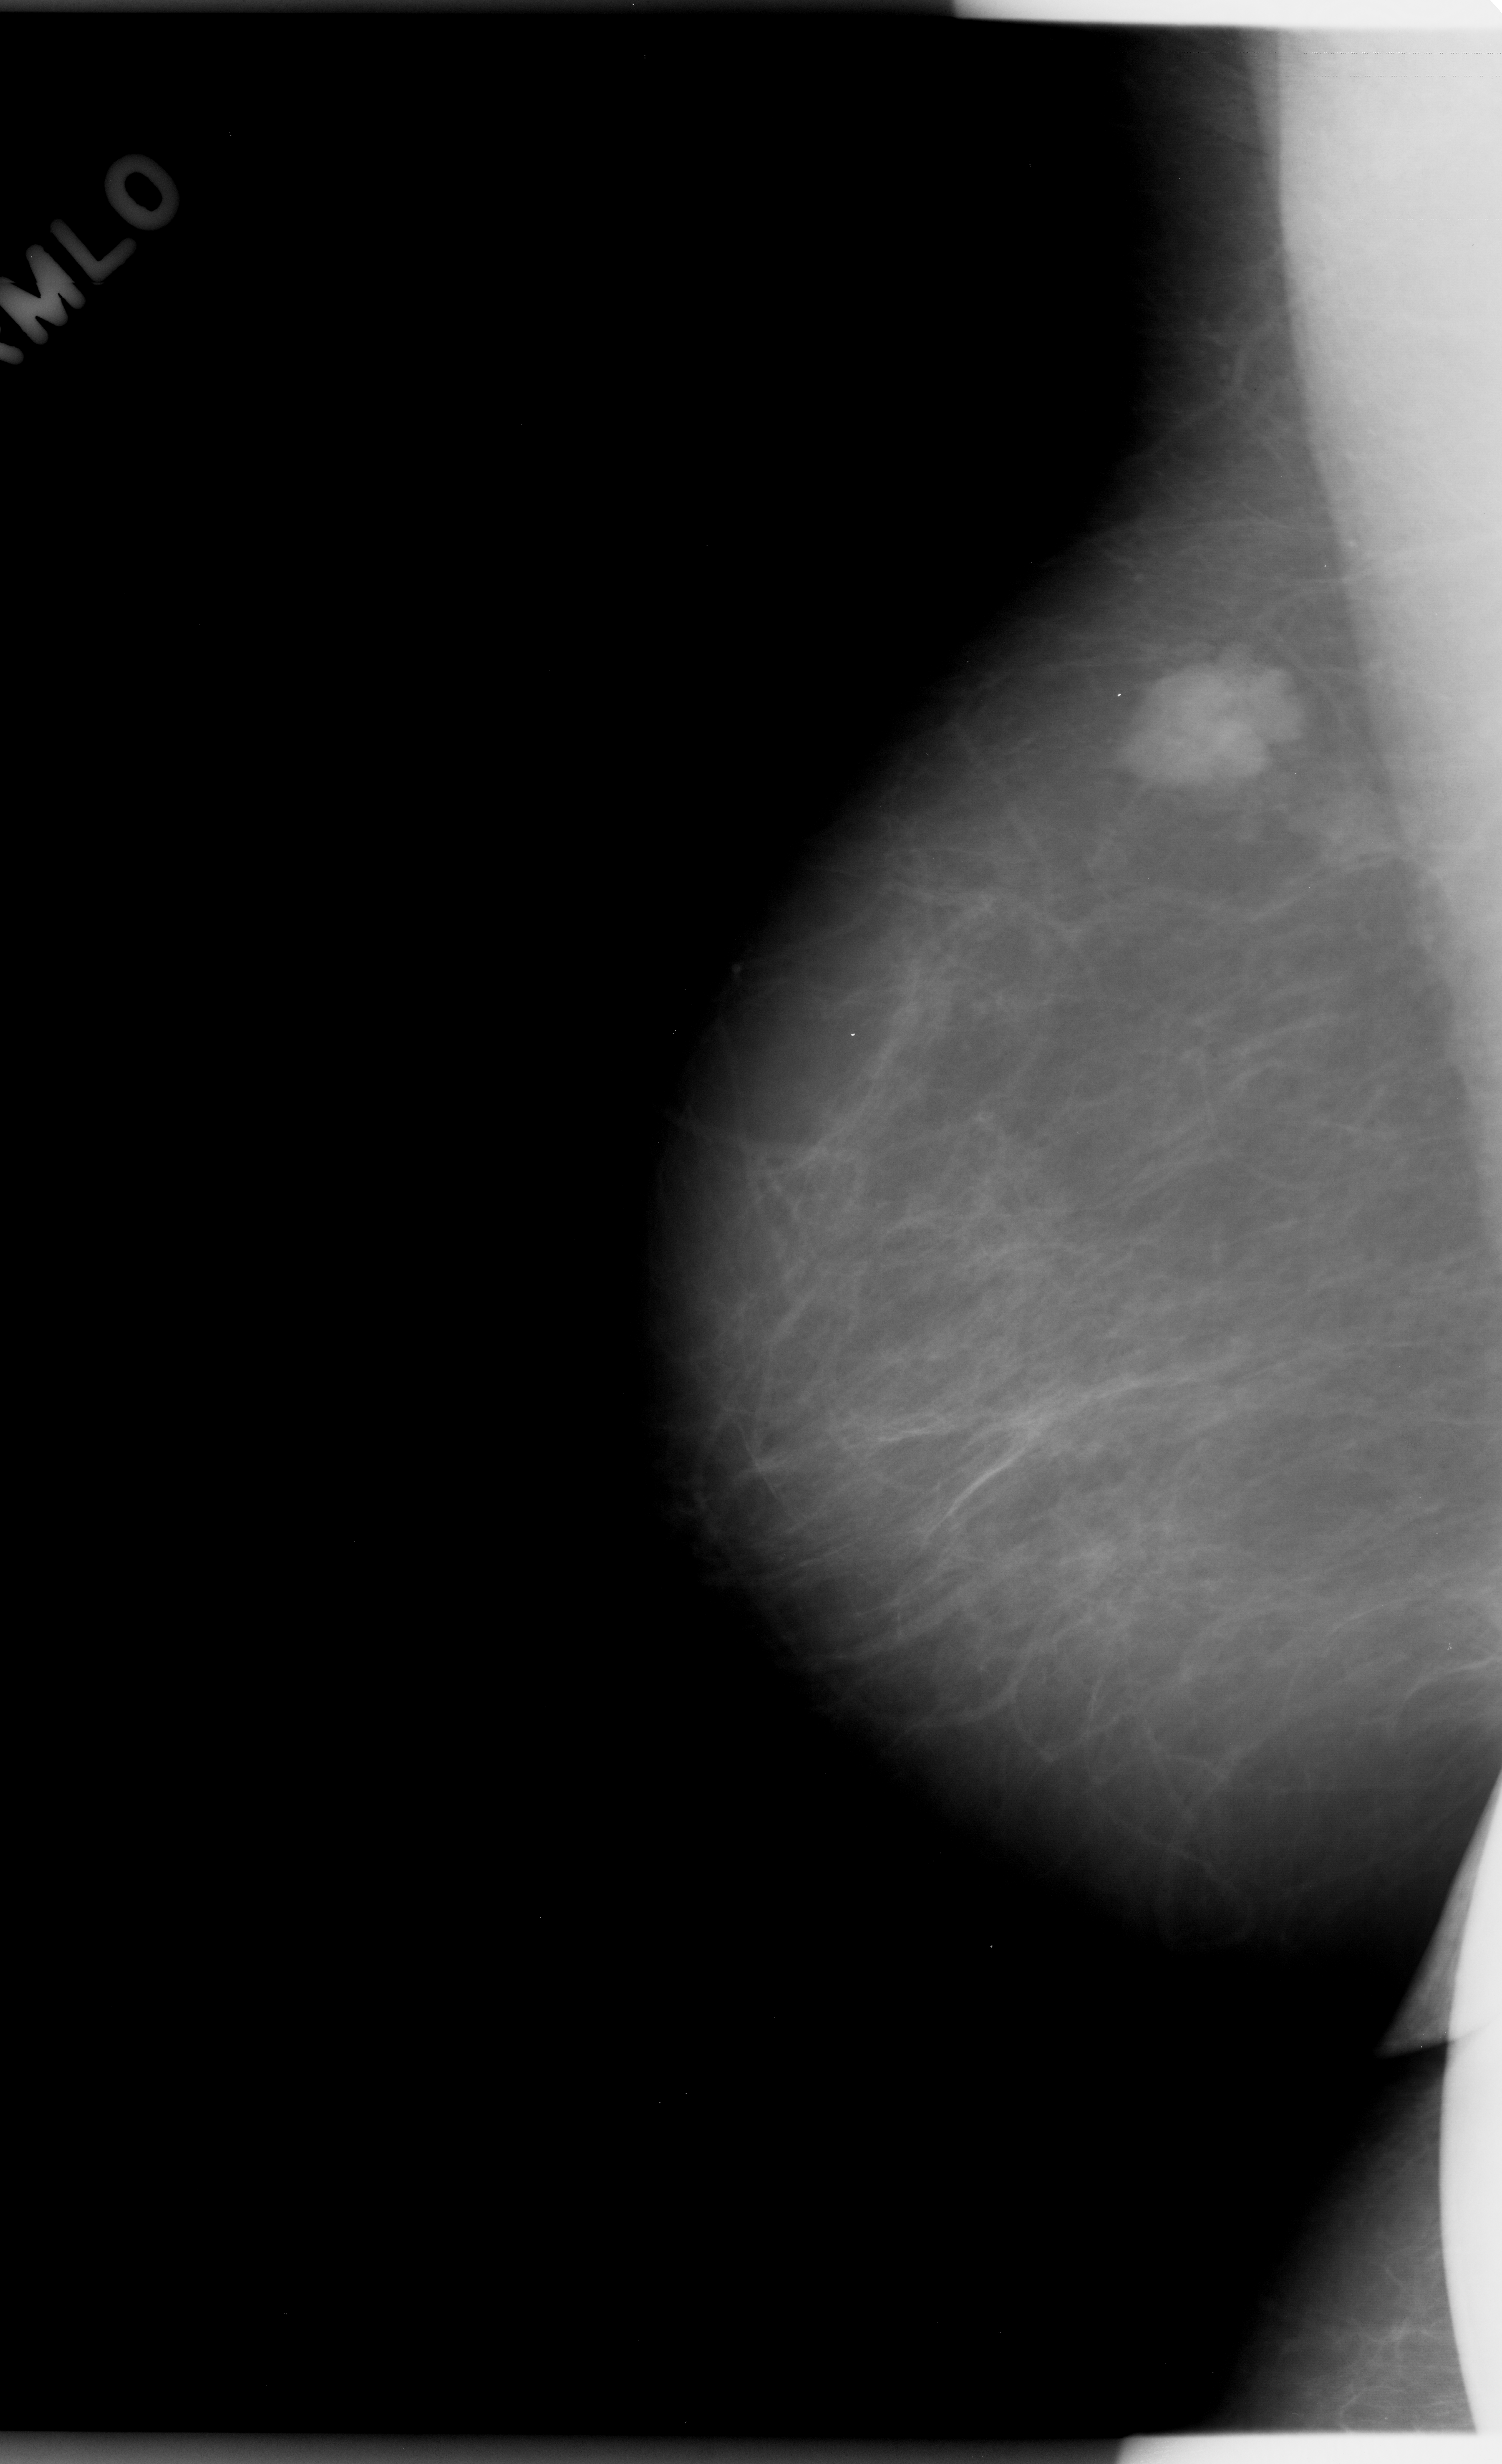
Digitized screen-film mammogram. Right breast. Mediolateral oblique (MLO) view. Breast composition: almost entirely fatty (BI-RADS density category 1 of 4). 1502 × 2464 image matrix.
Expert-marked regions of interest on this image (one box per marked abnormality):
- mass, shape lobulated, margins microlobulated; BI-RADS assessment category 5; subtlety rating 5 on a 1 (subtle) to 5 (obvious) scale; pathology (as recorded): malignant: bounding box <1099,636,1303,811> (left, top, right, bottom; pixels)